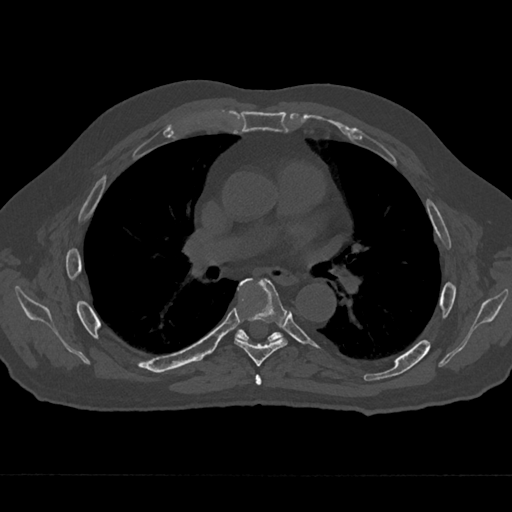
CT including the spine, one axial slice. Position 406 of 797 along the scan axis. Reconstruction kernel Br40s/3. 120 kVp. Bone window (W 1800 / L 400 HU). 0.5 mm slice thickness. 512 × 512 image matrix, field of view 377 × 377 mm. Patient: male, 75 years. From the clinical record (not read from this slice): primary cancer: renal; vertebrae with lytic lesions (as recorded): T4.
Outlined on this slice (semi-automatic segmentation, software-assisted and operator-edited):
- T5 vertebra: box from (x=255, y=375) to (x=262, y=385) px
- T6 vertebra: (x=234, y=278)–(x=288, y=366)
- T7 vertebra: (x=235, y=280)–(x=281, y=342)